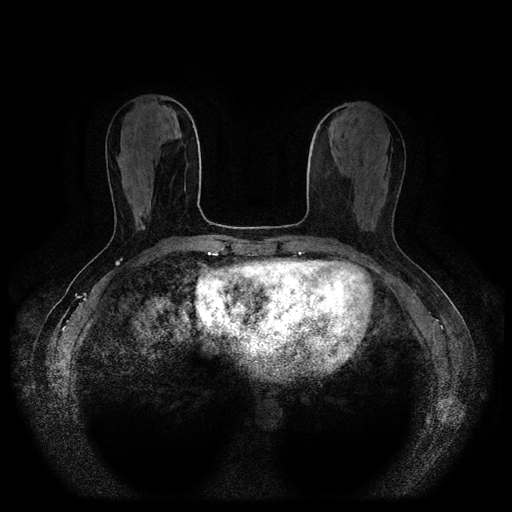
Breast MRI (dynamic contrast-enhanced, multi-phase), one axial slice. Position 35 of 116 along the scan axis. Dynamic contrast-enhanced series, time point 2 of 5 at this slice position (early post-contrast). 1.5 T. TE 2.6 ms, TR 5.3 ms. 2 mm slice thickness. 512 × 512 image matrix, field of view 360 × 360 mm. Female patient, age 53 years.
Structures marked on this image (semi-automatically segmented with operator editing):
- breast lesion (labelled 'tumour' in the annotation; benign lesions carry a separate 'benign' label): box from (x=135, y=211) to (x=145, y=230) px